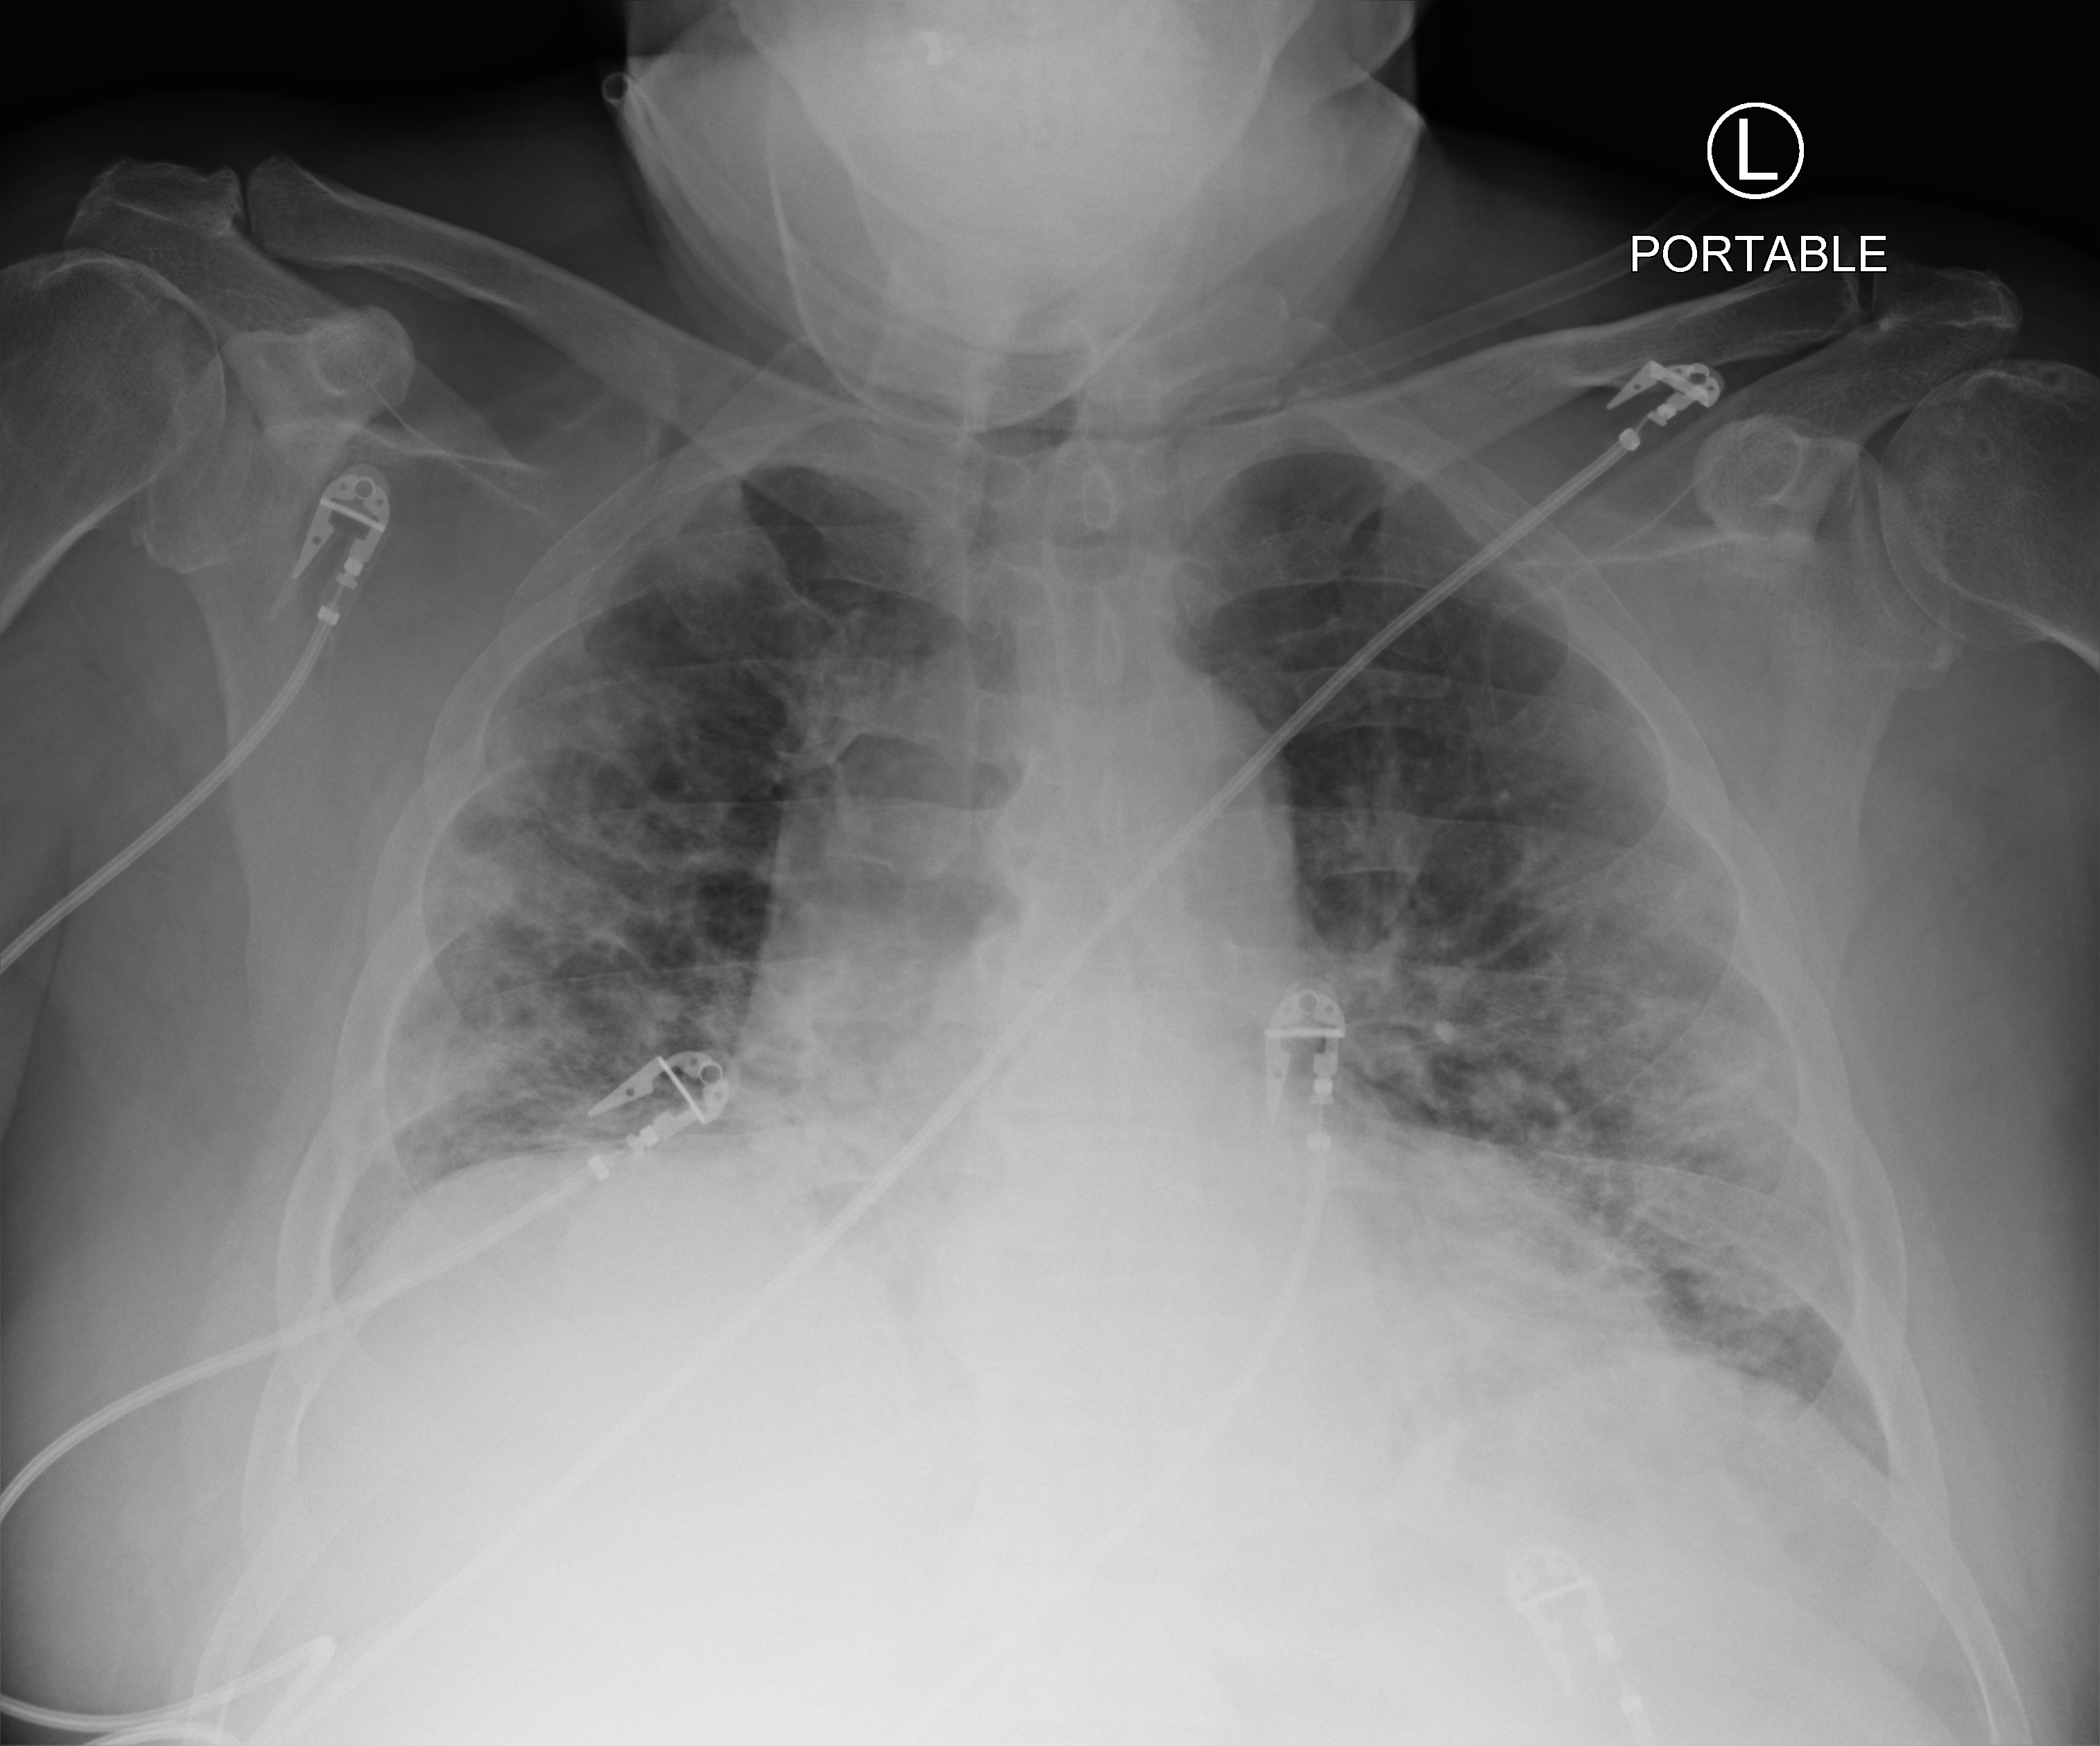
Portable chest radiograph, anteroposterior (AP) projection. Male patient hospitalised with COVID-19, age 60–74 years.
Hospital-stay facts (about this admission, not read from this image; timing relative to this image not recorded):
- admitted to intensive care during this hospital stay: no
- mechanically ventilated during this hospital stay: no